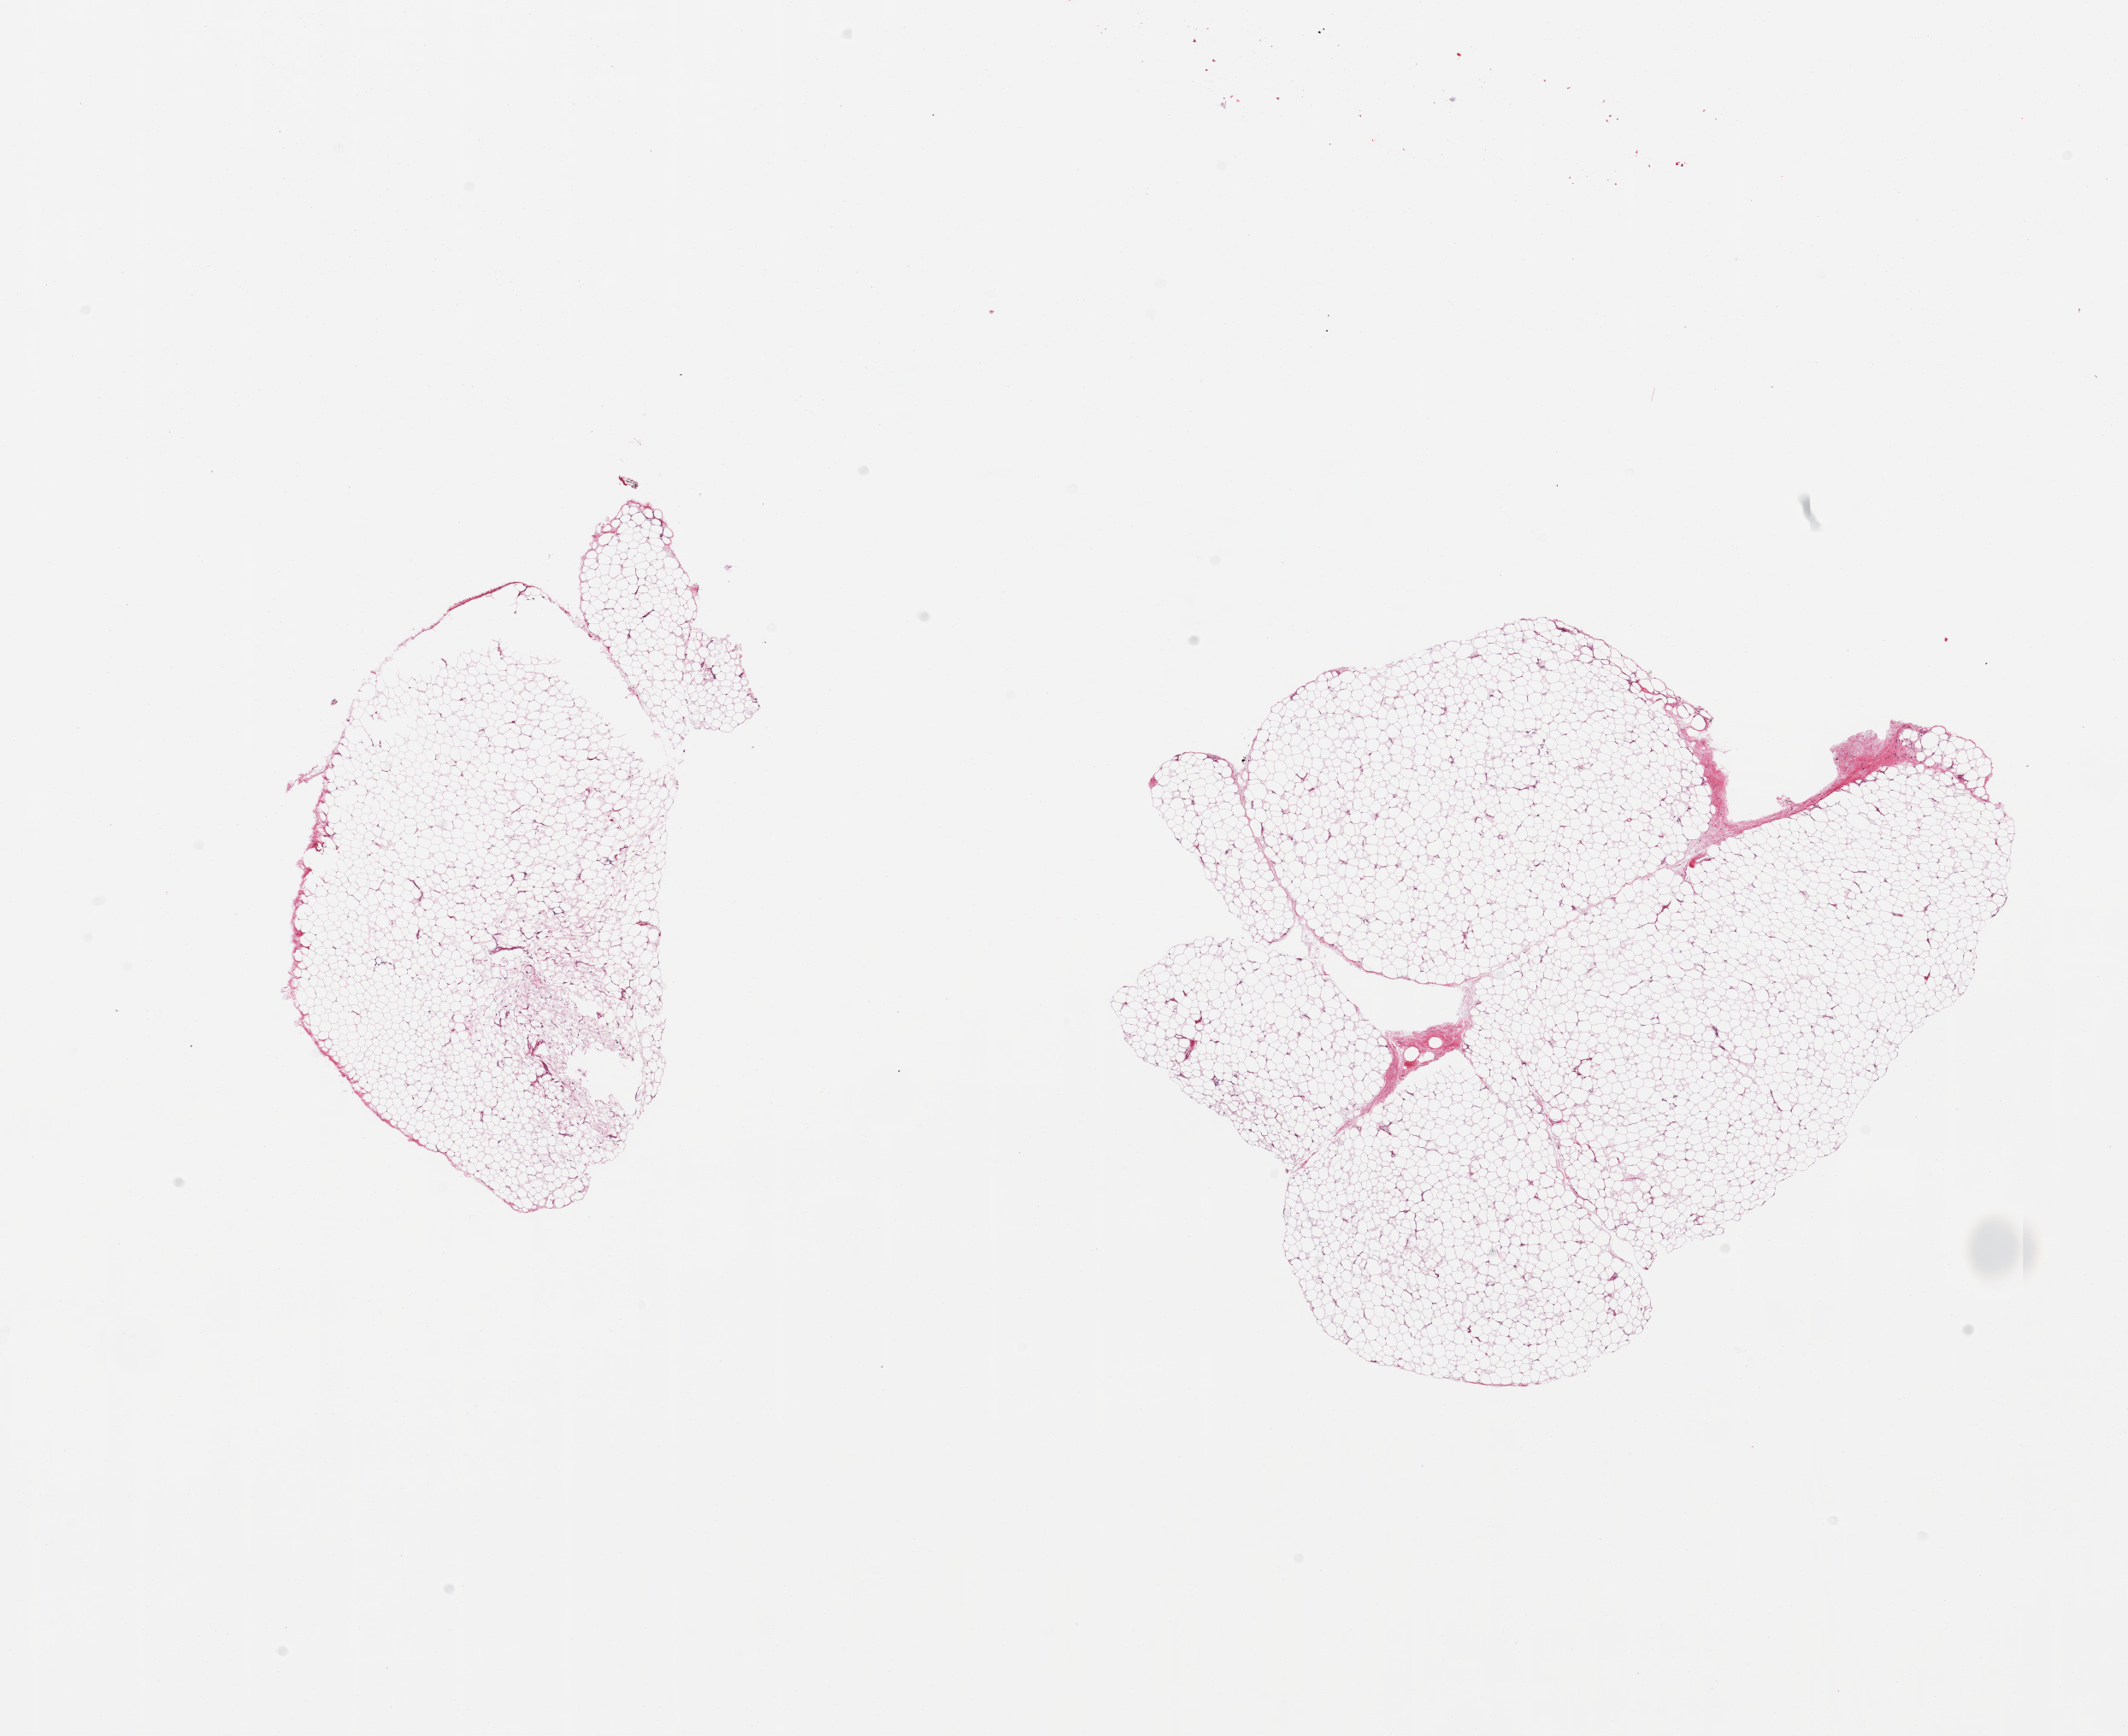
Whole-slide image, hematoxylin and eosin (H&E) stain, low-resolution overview of the scanned area, about 19.7 x 16.1 mm. PAXgene-fixed paraffin-embedded (PFPE) section. Sampled site (target tissue): adipose tissue. Tissue donor sample. Donor sex: female.
Review note (as recorded): 2 pieces, trace fascia.